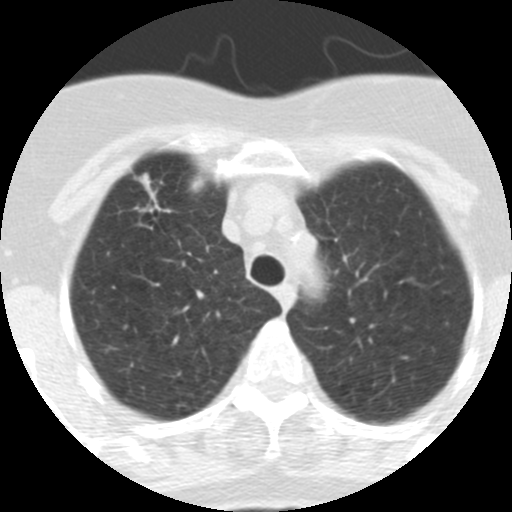
Axial slice from a low-dose chest CT screening exam, baseline screening round, lung window (W 1500 / L -600 HU), slice 63 of 313 in the series. Female participant, aged 62 years at enrolment. Current smoker at enrolment.
- Expert-annotated lung lesion, bounding box (x1, y1, x2, y2) in pixels: (116, 169, 188, 237).
- Reader record for this screening exam (exam-level; its link to the box is not recorded): non-calcified nodule or mass ≥4 mm, right upper lobe, 9 × 7 mm, spiculated (stellate) margins, soft tissue attenuation.
- Lung cancer was diagnosed 126 days after this screen: adenocarcinoma, NOS, right upper lobe, moderately differentiated (G2), stage IA (AJCC 6th edition), 18 mm at pathology.